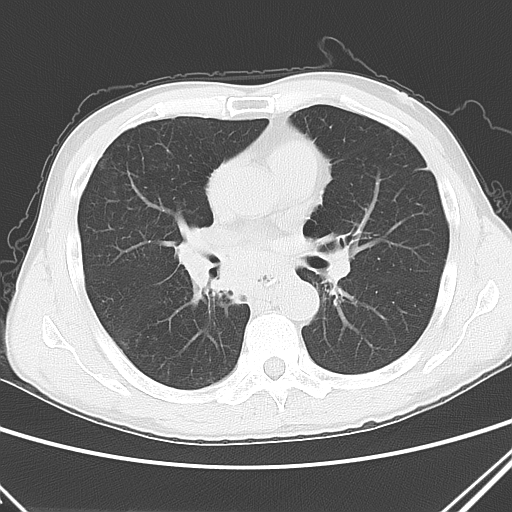
Chest CT, one axial slice; lung window (W 1500 / L -600 HU); 5 mm slice thickness; 512 × 512 image matrix, field of view 327 × 327 mm. Male patient, age 52 years. From the clinical record (not read from this slice): clinical TNM (as recorded): T2a N0 M1c.
Structures marked on this image (bounding box drawn by a radiologist):
- lung tumour (recorded histology: squamous cell carcinoma): bounding box [x1, y1, x2, y2] px = [173, 224, 245, 320]